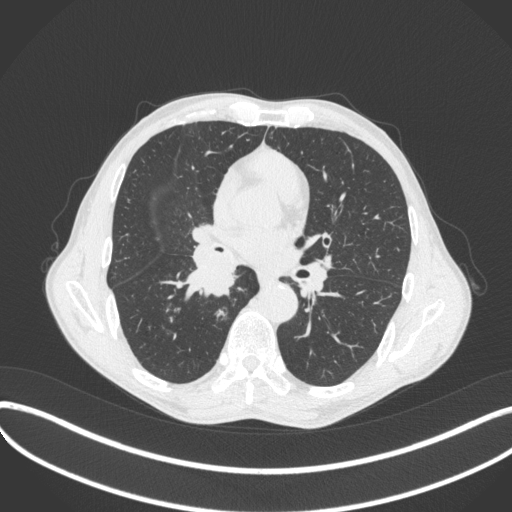
Chest CT, one axial slice; slice 224 of 481 in the series (ordered by position); reconstruction kernel B31f; lung window (W 1500 / L -600 HU); 512 × 512 image matrix. Patient: male, 65 years. Case-level facts recorded for this patient, not image findings: clinical TNM (as recorded): T2a N0 M0.
Outlined on this slice (bounding box drawn by a radiologist):
- lung tumour (recorded histology: squamous cell carcinoma): bounding box (x1, y1, x2, y2) in pixels: (173, 239, 243, 307)